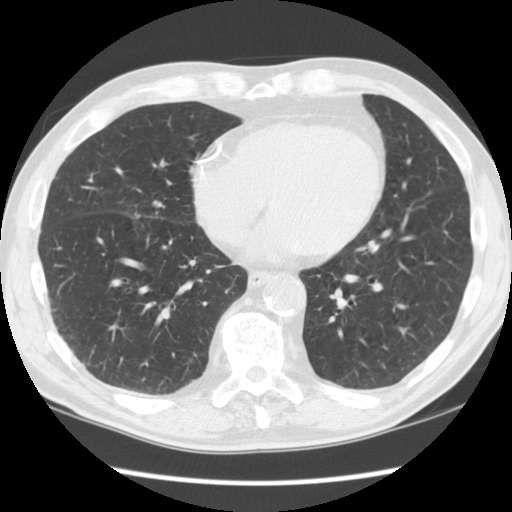
Axial slice from a low-dose chest CT screening exam. Second annual screen. Lung window (W 1500 / L -600 HU). Standard (soft-tissue) reconstruction kernel (STANDARD). 120 kVp. Slice 85 of 132 in the series. Male, age 64 years at enrolment.
Expert-annotated lung lesion, bounding box (x1, y1, x2, y2) in pixels: (130, 193, 177, 229). The exam's reader record, not a measurement of the box and not confirmed to be the same lesion: non-calcified nodule or mass ≥4 mm, right middle lobe, 6 × 5 mm, smooth margins, soft tissue attenuation, pre-existing on the prior screen: no. Official screen result: positive, other. Lung cancer was diagnosed 300 days after this screen (after the third annual screen): non-small cell carcinoma, right middle lobe, poorly differentiated (G3), stage IIIA (AJCC 6th edition), 20 mm at pathology.